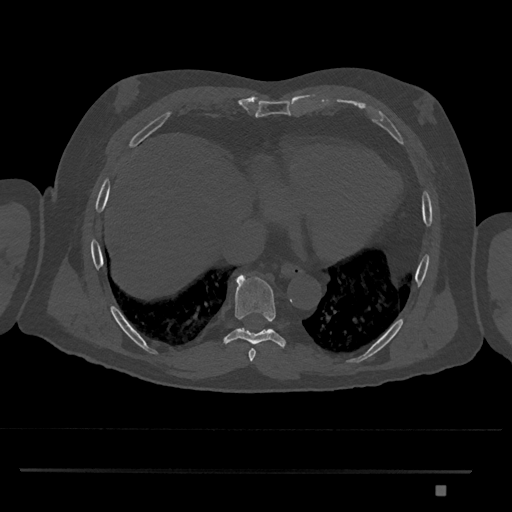
CT including the spine, one axial slice; position 1110 of 1134 along the scan axis; reconstruction kernel Br40s/3; bone window (W 1800 / L 400 HU); 0.5 mm slice thickness; 512 × 512 image matrix. Male patient, age 65 years. From the clinical record (not read from this slice): primary cancer: prostate.
Structures marked on this image (semi-automatic segmentation, software-assisted and operator-edited):
- T8 vertebra: bounding box (x1, y1, x2, y2) in pixels: (224, 274, 285, 347)